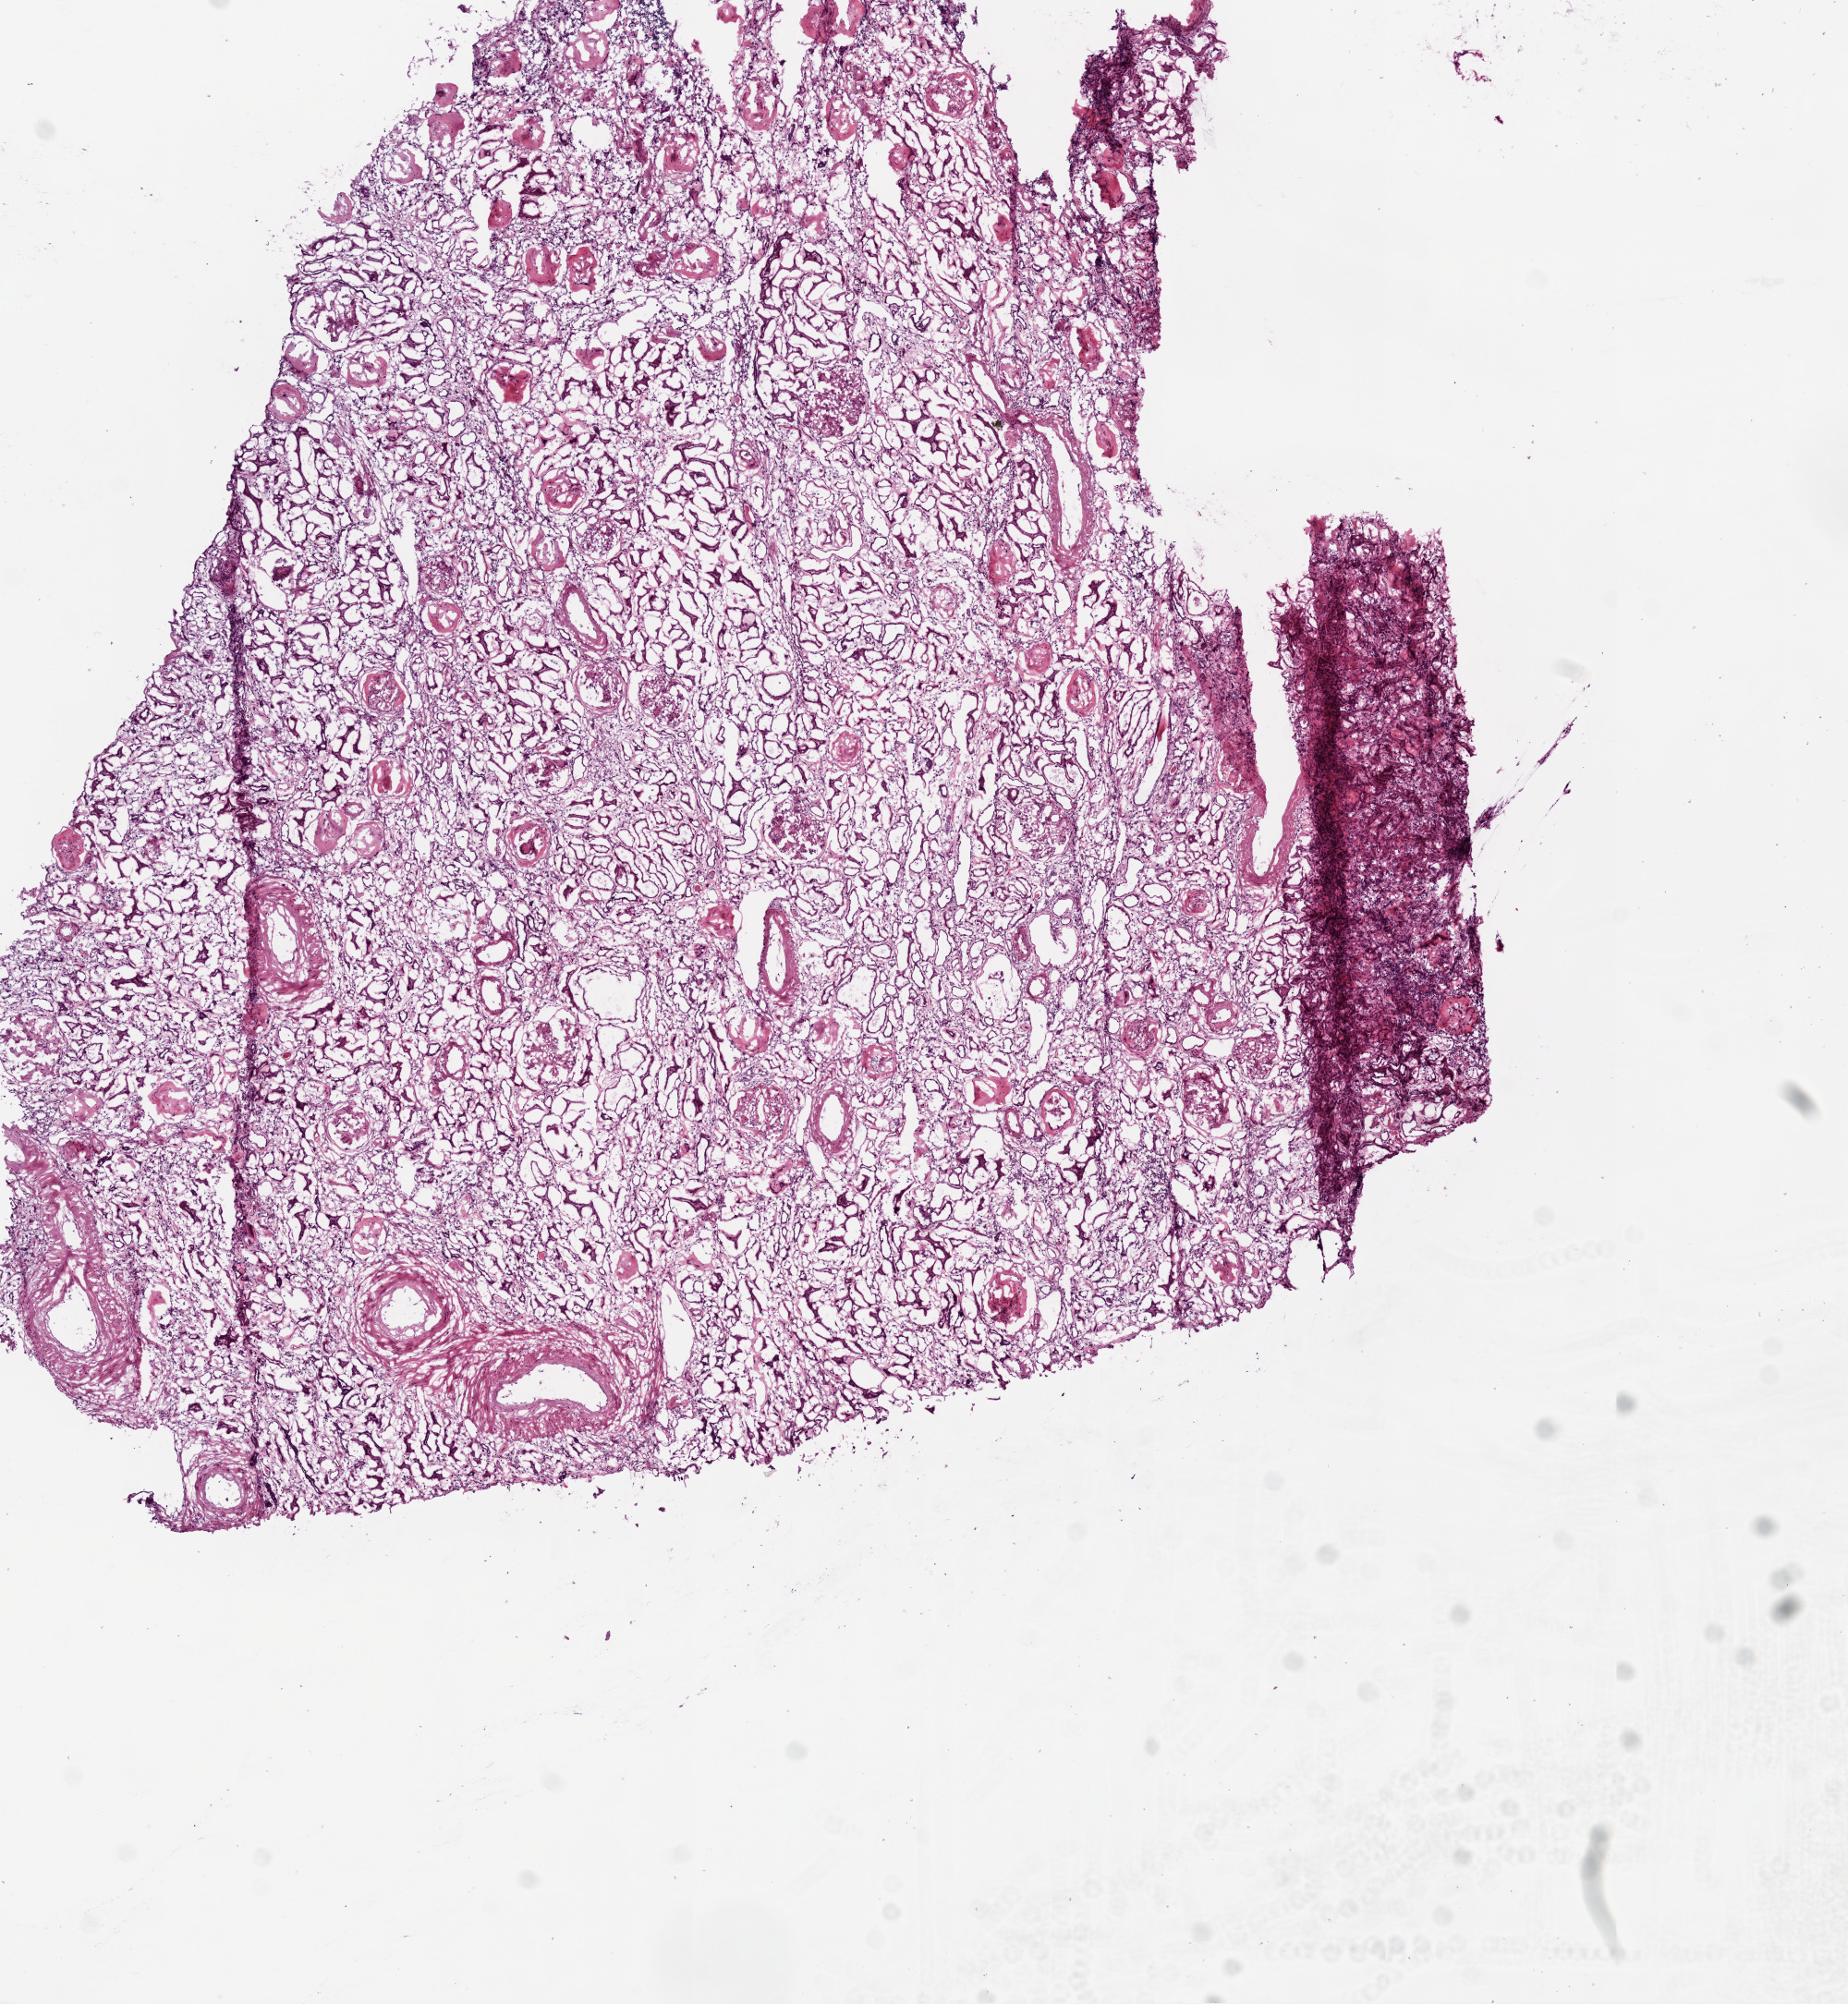
Digitized H&E tissue section (whole slide), shown as a low-resolution overview of the whole scanned area (about 8.0 x 8.7 mm), frozen section, solid tissue normal (non-tumour tissue) sample from the kidney. Female patient; age at initial diagnosis 70 years.
This section: solid tissue normal (non-tumour) sample from the same patient. Patient diagnosis: Clear cell adenocarcinoma, NOS.